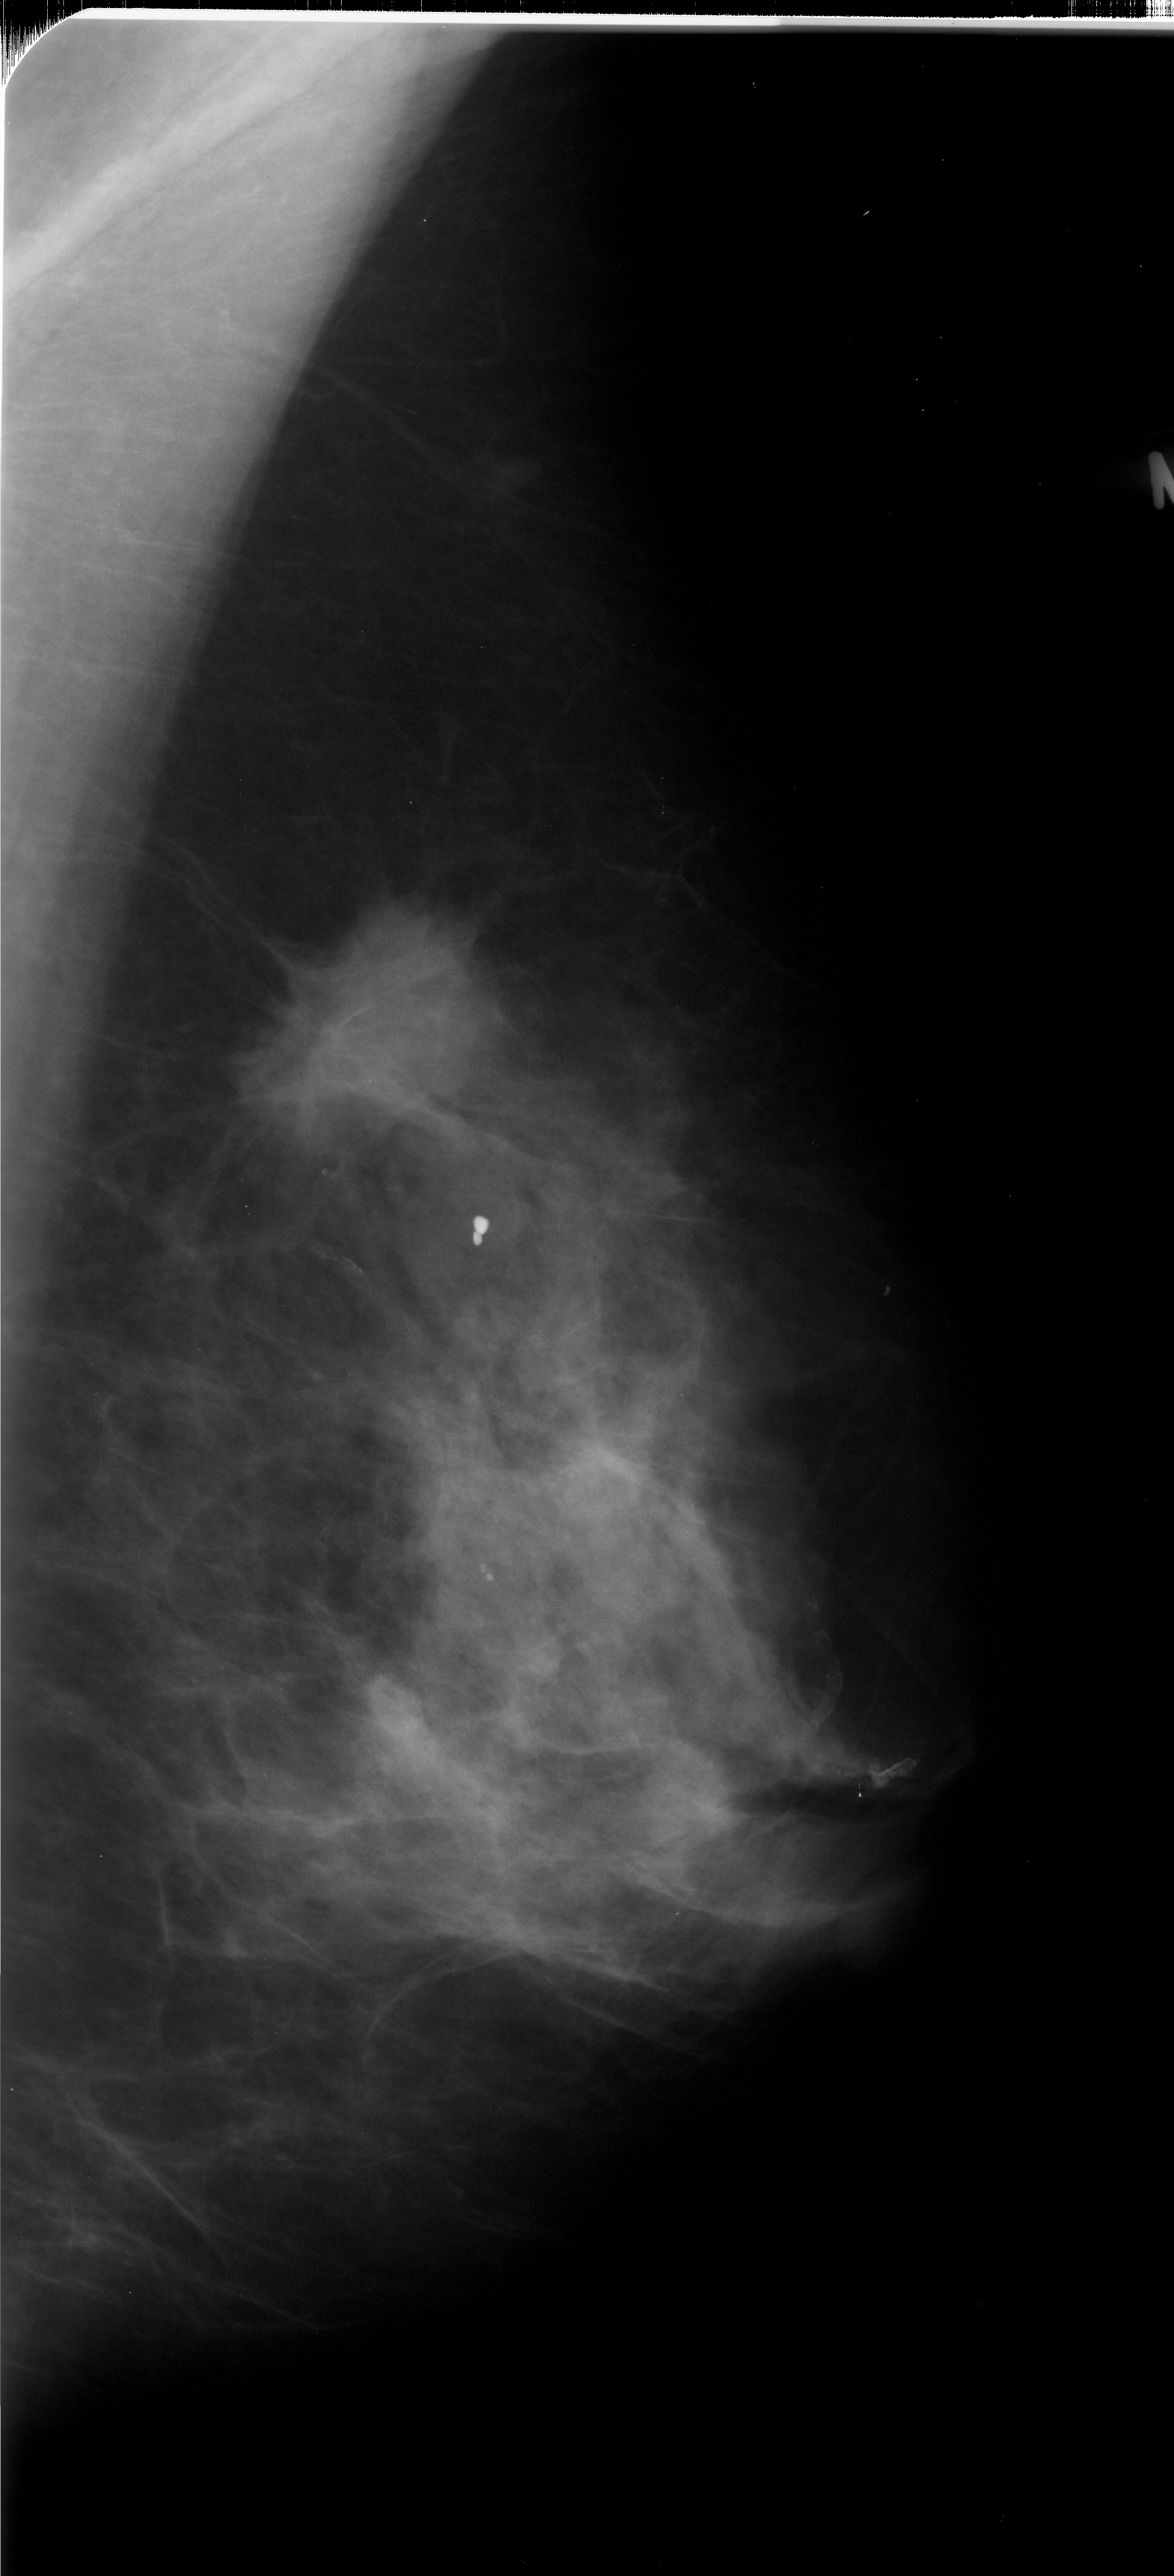
Scanned film-screen mammogram; right breast; mediolateral oblique (MLO) view; BI-RADS breast density category 3 (scale 1–4).
Abnormality record for this image: mass, shape irregular, margins spiculated; BI-RADS assessment category 5; pathology result (as recorded, not read from the image): malignant.